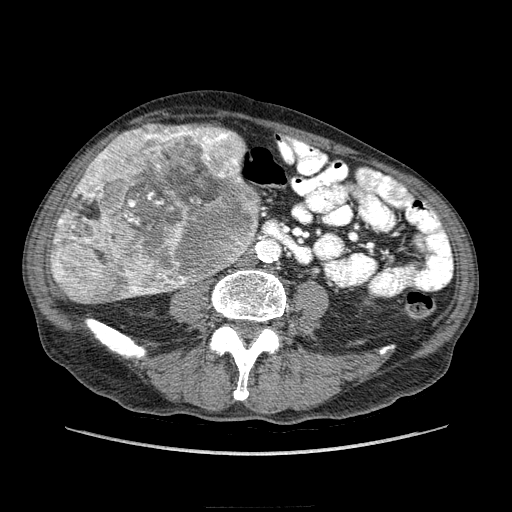
Contrast-enhanced abdominal CT (liver protocol), one axial slice. Position 53 of 218 along the scan axis. Soft-tissue window (W 400 / L 40 HU). 2.5 mm slice thickness. 512 × 512 image matrix, field of view 380 × 380 mm. Case-level facts recorded for this patient, not image findings: diagnosis: hepatocellular carcinoma (patient treated with transarterial chemoembolisation; whether this scan precedes or follows treatment is not stated here); TNM stage (as recorded): Stage-IIIA; Child-Pugh class: A; tumour differentiation: well differentiated; tumour nodularity: multinodular.
Structures marked on this image (semi-automatically segmented with operator editing):
- liver parenchyma outside the tumour (the mass and vessels are separate outlines, so this box may not span the whole liver): bounding box <50,126,258,298> (left, top, right, bottom; pixels)
- mass: <51,123,259,305>